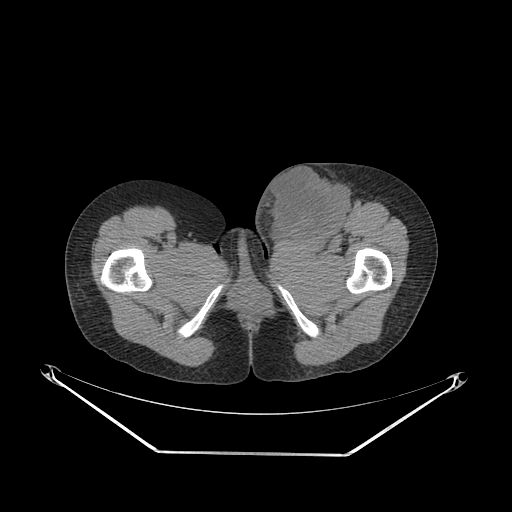
CT of an extremity soft-tissue mass (from a PET/CT study), one axial slice. Position 53 of 267 along the scan axis. Reconstruction kernel SOFT. 140 kVp. Soft-tissue window (W 400 / L 40 HU). 512 × 512 image matrix. Female patient. From the clinical record (not read from this slice): histological type: leiomyosarcoma; grade: high; site of the primary tumour: groin.
Outlined on this slice (expert contour drawn on MRI and transferred to this co-registered scan by the dataset authors):
- gross tumour volume including surrounding oedema: bounding box (x1, y1, x2, y2) in pixels: (251, 162, 364, 241)
- gross tumour volume (mass): (269, 167, 348, 241)